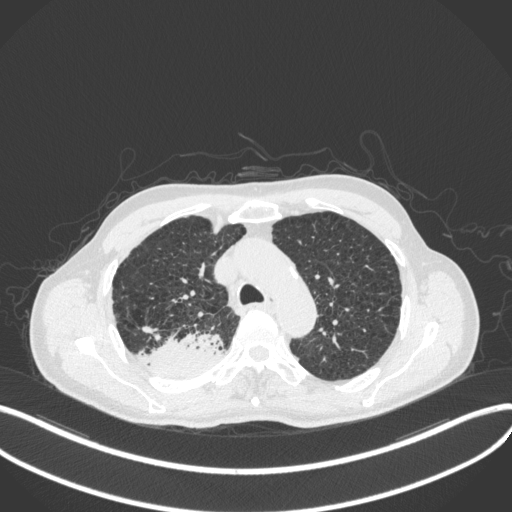
Chest CT, one axial slice. Slice 328 of 423 in the series (ordered by position). Reconstruction kernel B31f. Lung window (W 1500 / L -600 HU). 1 mm slice thickness. 512 × 512 image matrix, field of view 400 × 400 mm. Male patient, age 79 years. Case-level facts recorded for this patient, not image findings: clinical TNM (as recorded): T3 N0 M0.
Structures marked on this image (bounding box drawn by a radiologist):
- lung tumour (recorded histology: adenocarcinoma): bounding box [x1, y1, x2, y2] px = [150, 332, 221, 382]